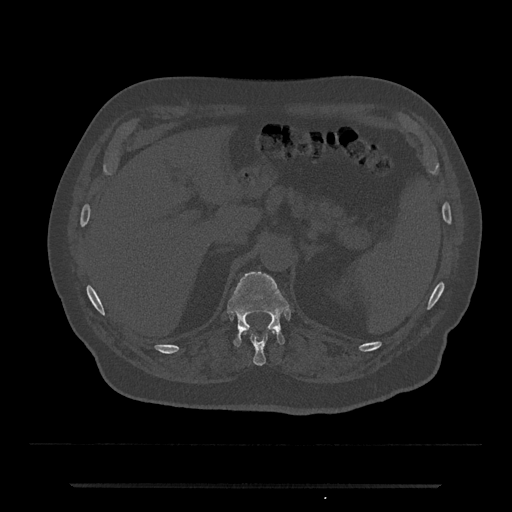
CT including the spine, one axial slice. Slice 614 of 797 in the series (ordered by position). Reconstruction kernel Br40s/3. 120 kVp. Bone window (W 1800 / L 400 HU). 512 × 512 image matrix, field of view 434 × 434 mm. Patient: male, 80 years. From the clinical record (not read from this slice): primary cancer: prostate; vertebrae with lytic lesions (as recorded): L1, T11.
Annotated regions visible in this slice (semi-automatically segmented with operator editing):
- T11 vertebra: bounding box (x1, y1, x2, y2) in pixels: (250, 334, 267, 366)
- T12 vertebra: (228, 271, 289, 347)